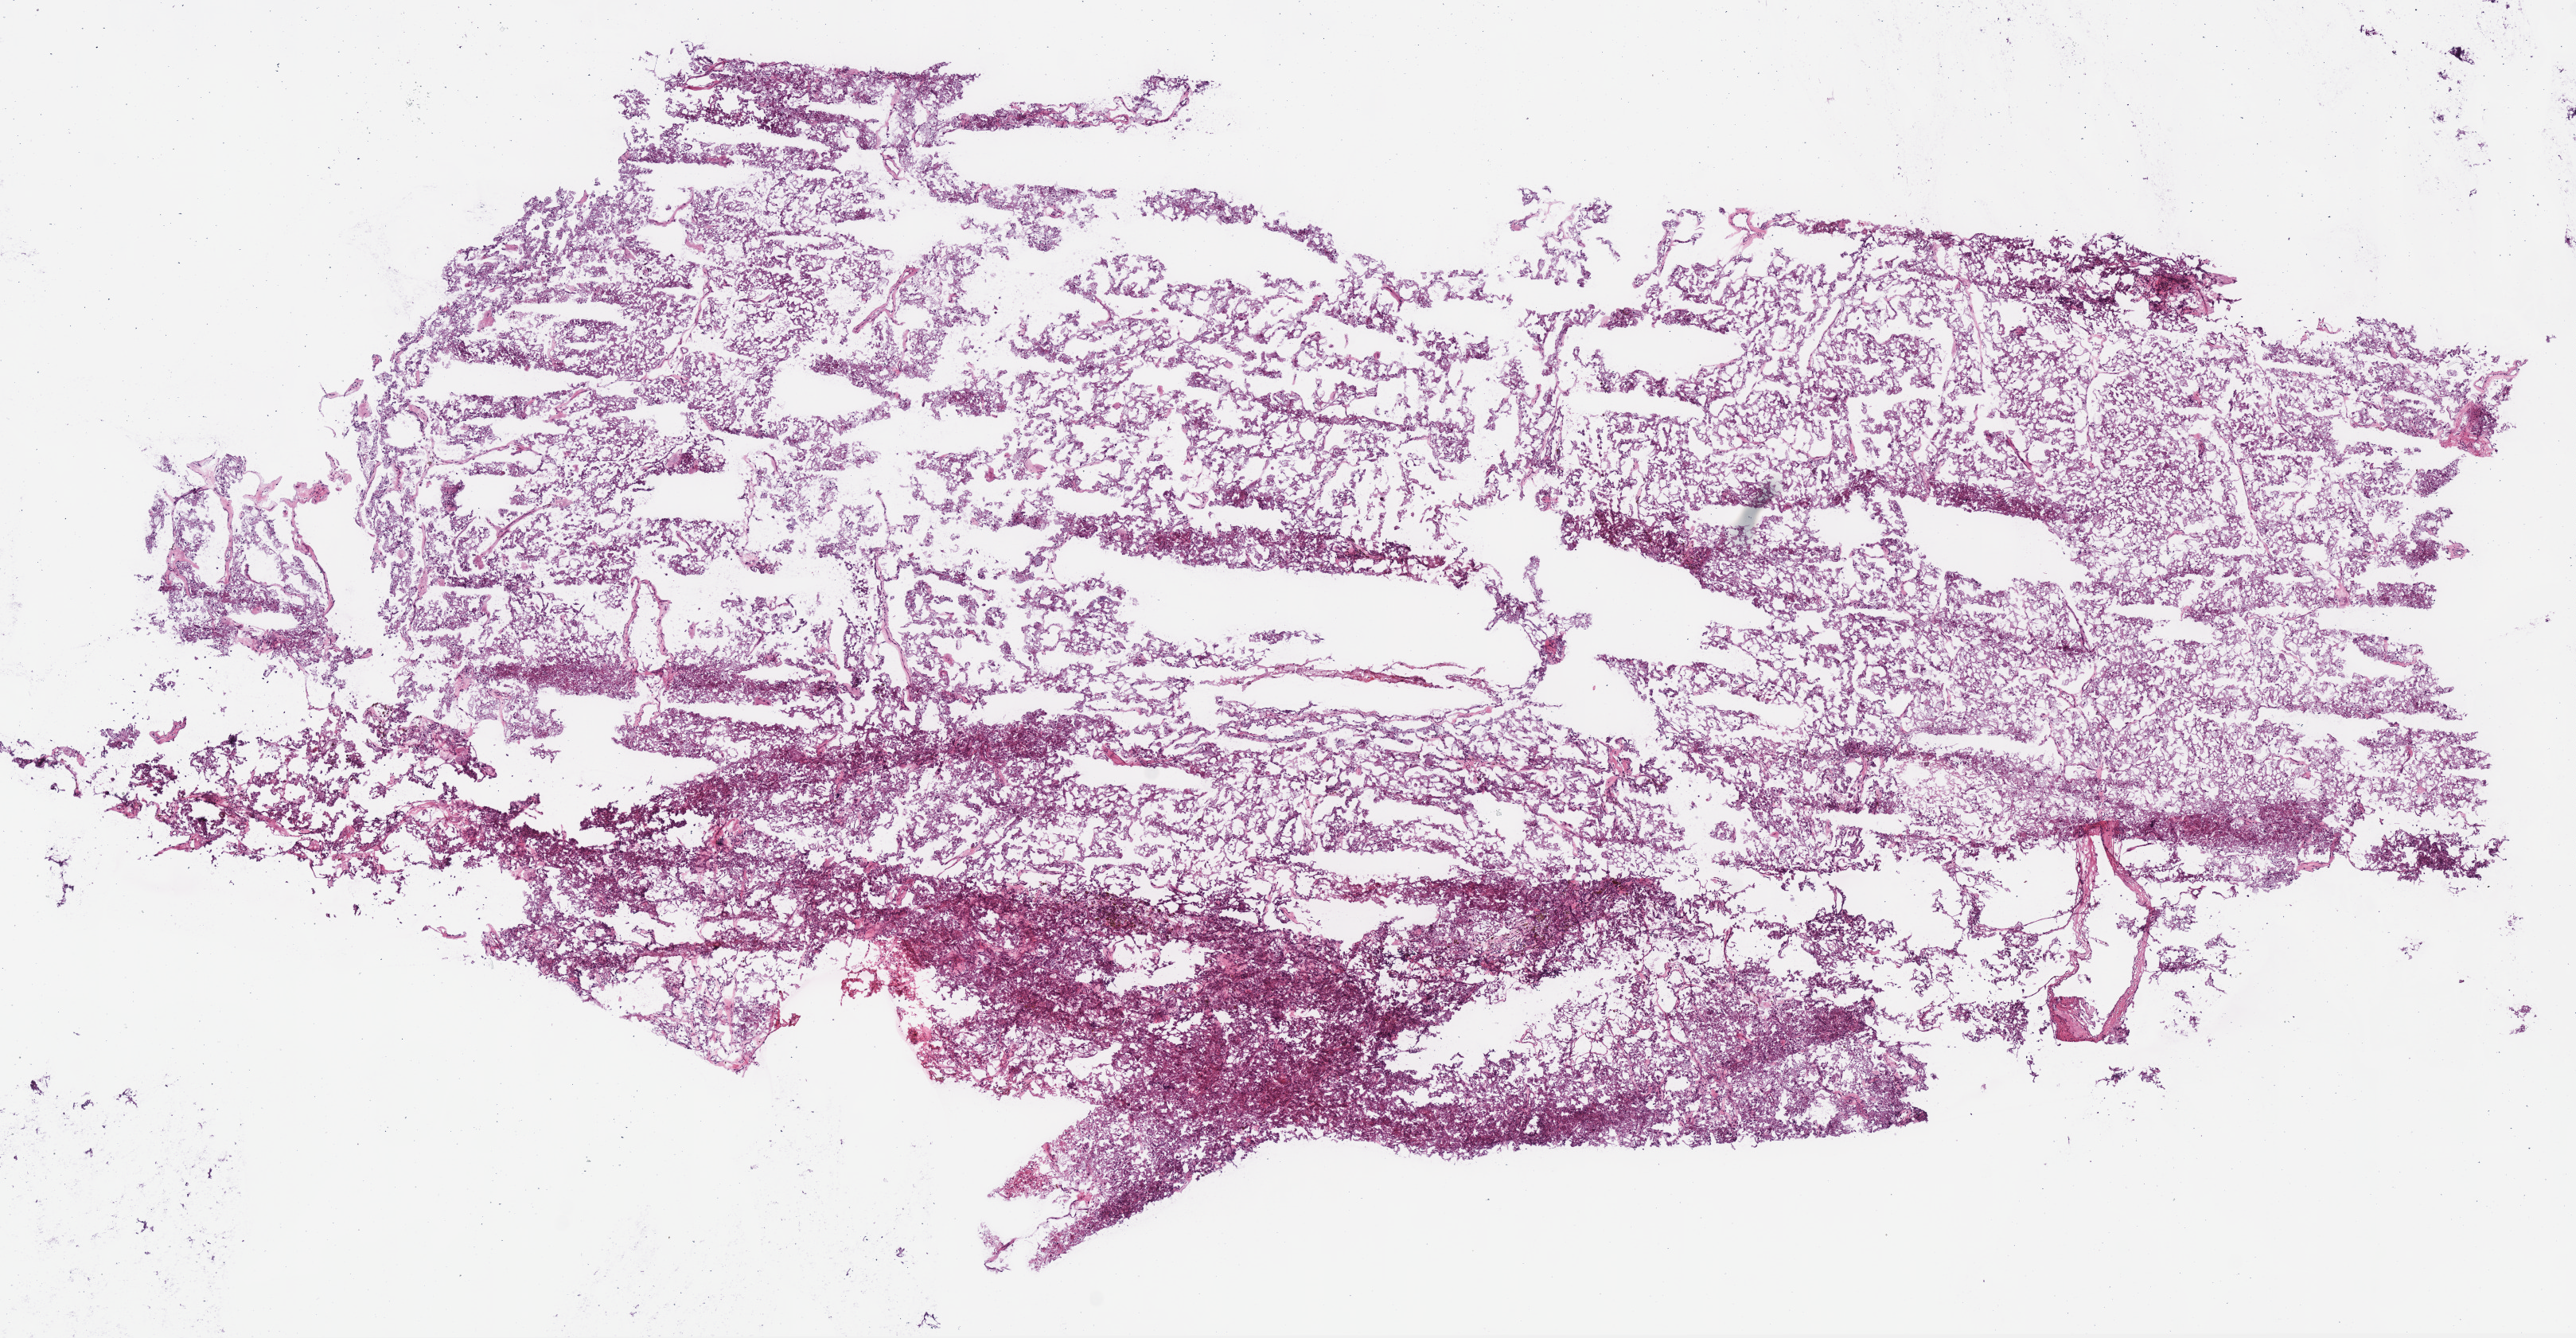
Whole-slide histology image, Hematoxylin and eosin (H&E) stained — shown as a low-resolution overview of the whole scanned area (about 12.7 x 6.6 mm, slide scanned at 40x); frozen section from the bottom of the tissue portion; sample: primary tumour, kidney. Male, age 51 years at initial diagnosis. Pathologist review of this section (percent, as recorded): tumour cells 95%, tumour nuclei 95%, normal cells 0%, stromal cells 5%, necrosis 0%.
* laterality: left
* histologic diagnosis: Renal cell carcinoma, chromophobe type
* AJCC pathologic stage: III (6th edition)